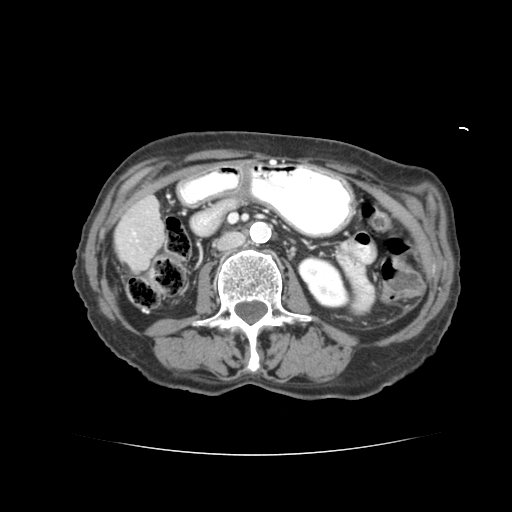
Contrast-enhanced abdominal CT (liver protocol), one axial slice; slice 12 of 77 in the series (ordered by position); reconstruction kernel STANDARD; soft-tissue window (W 400 / L 40 HU); 2.5 mm slice thickness; 512 × 512 image matrix, field of view 340 × 340 mm. Case-level facts recorded for this patient, not image findings: diagnosis: hepatocellular carcinoma (patient treated with transarterial chemoembolisation; whether this scan precedes or follows treatment is not stated here); TNM stage (as recorded): Stage-I; Child-Pugh class: A.
Structures marked on this image (semi-automatic segmentation, software-assisted and operator-edited):
- liver parenchyma outside the tumour (the mass and vessels are separate outlines, so this box may not span the whole liver): bounding box <114,186,160,268> (left, top, right, bottom; pixels)
- liver vessels: <134,209,153,239>